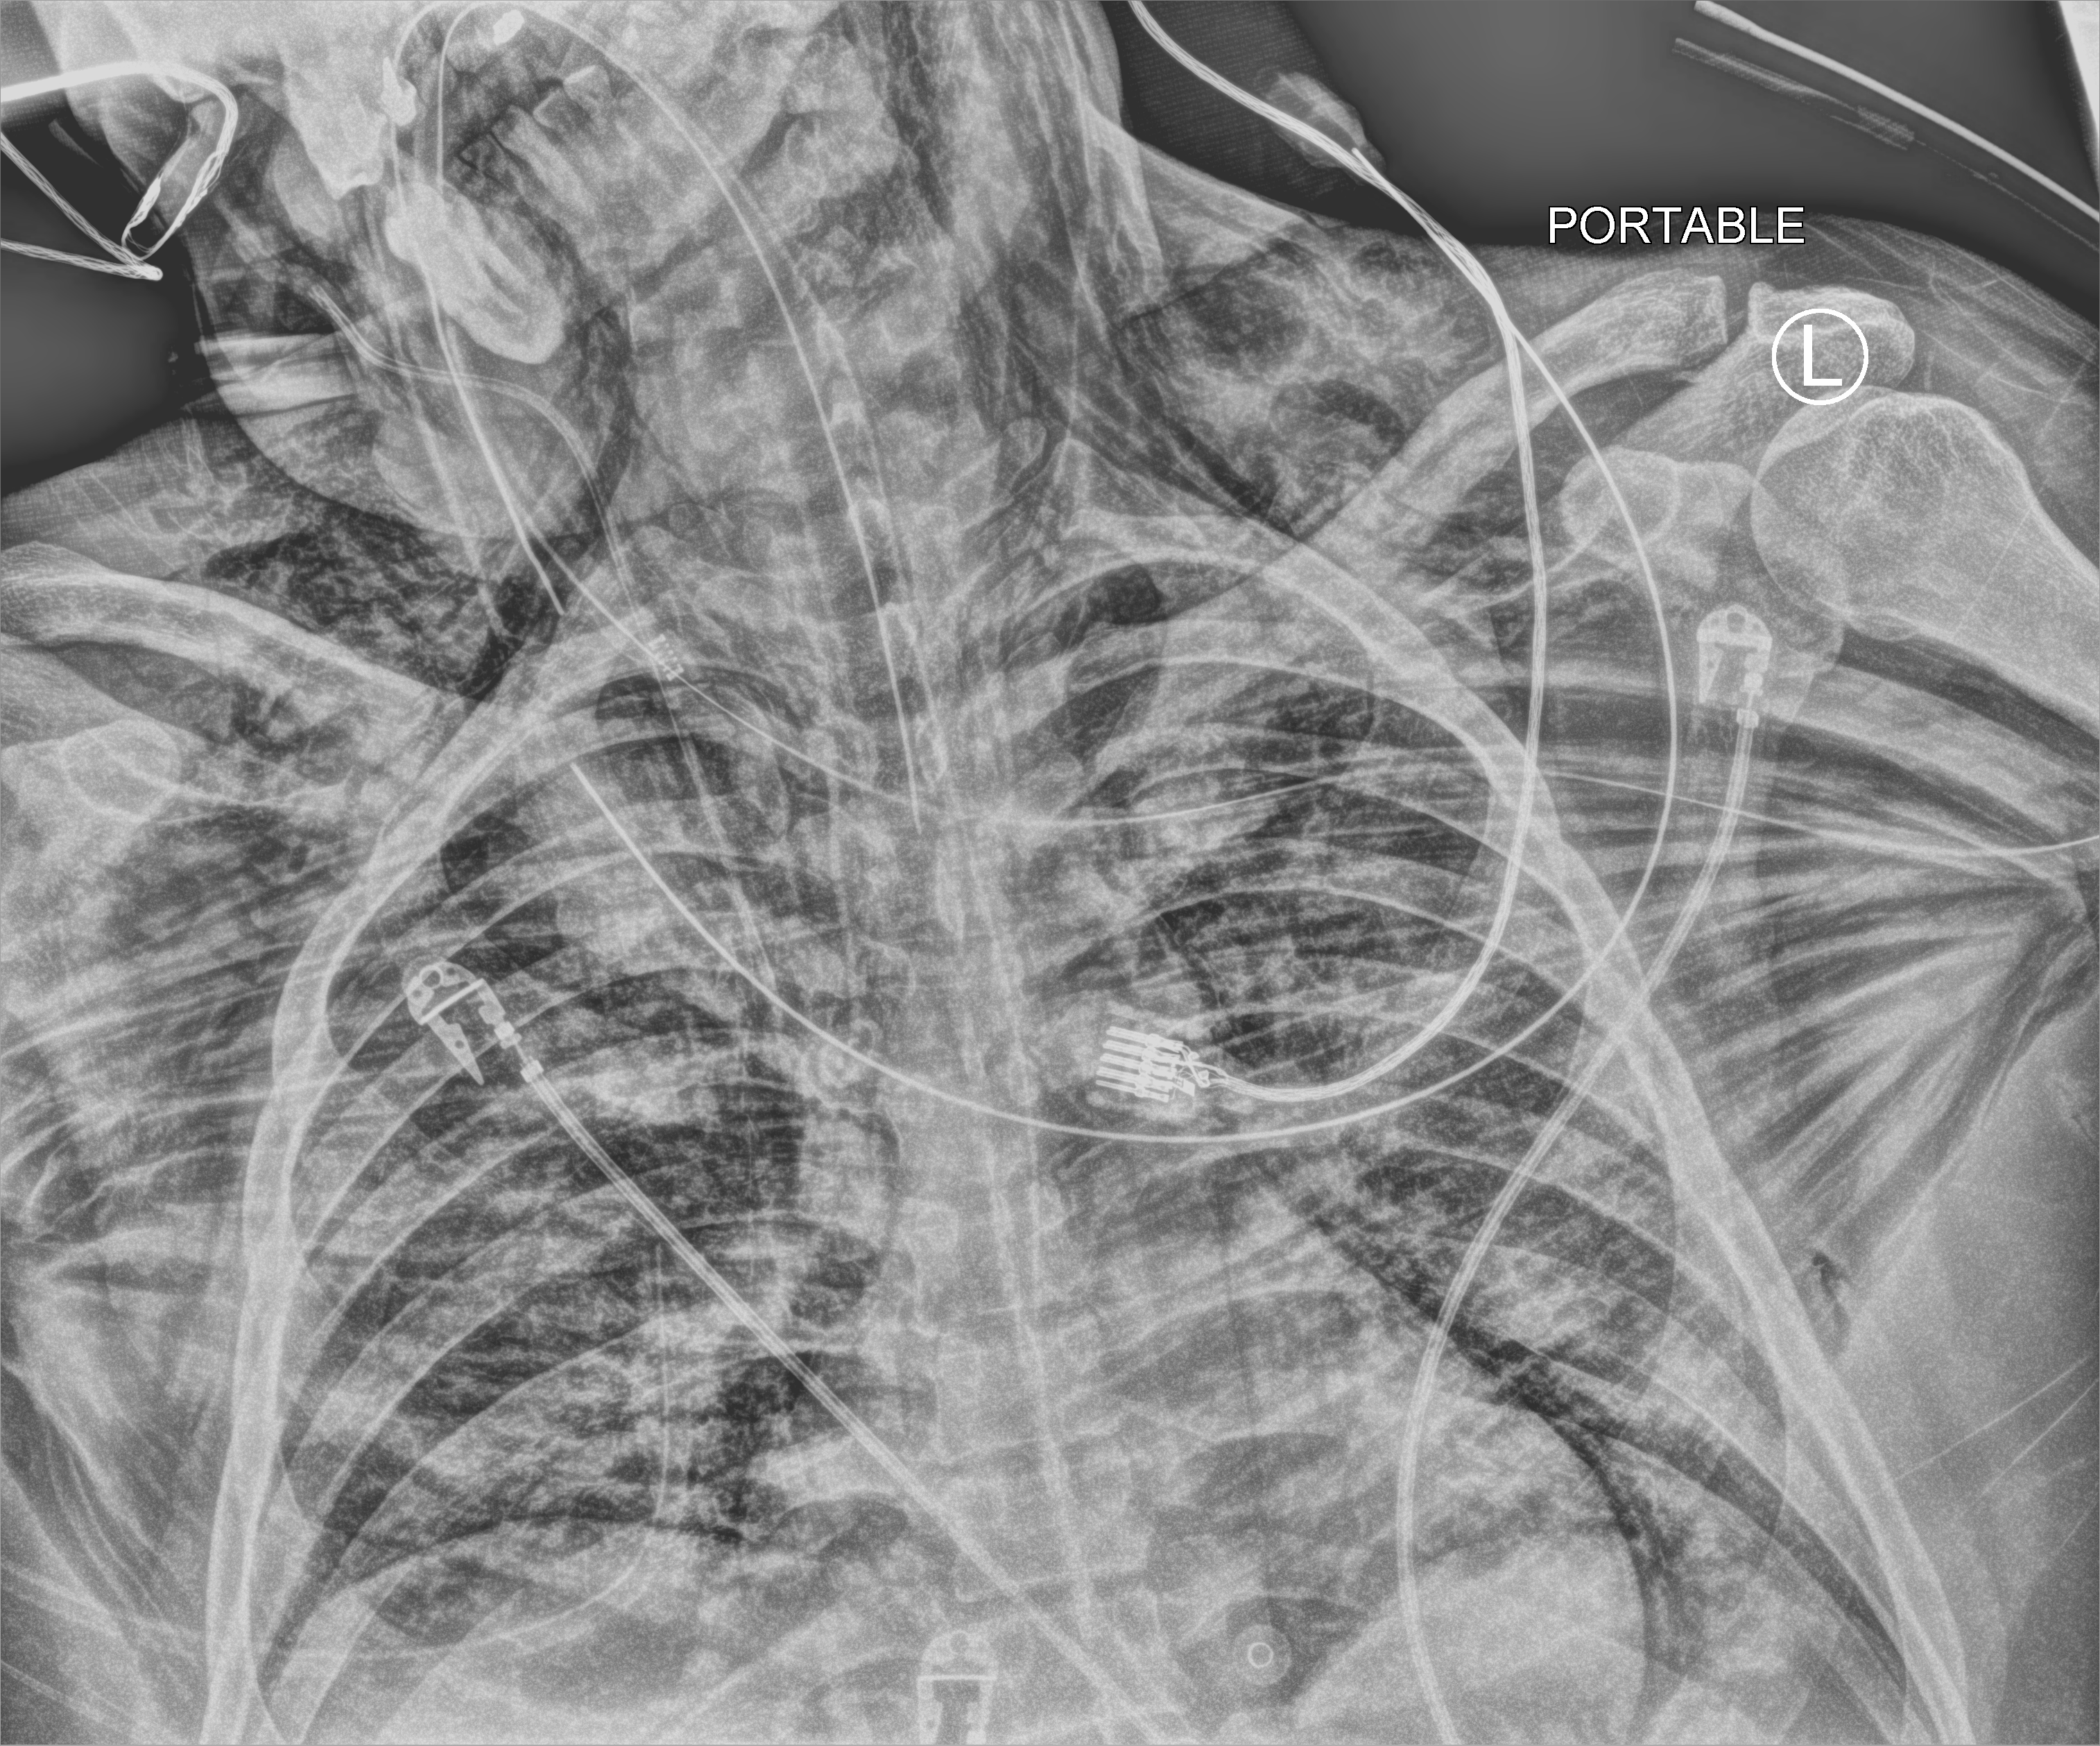
Chest X-ray (portable). Patient hospitalised with COVID-19; male, aged 18–59 years.
Hospital-stay facts (about this admission, not read from this image; timing relative to this image not recorded):
- admitted to intensive care during this hospital stay: yes